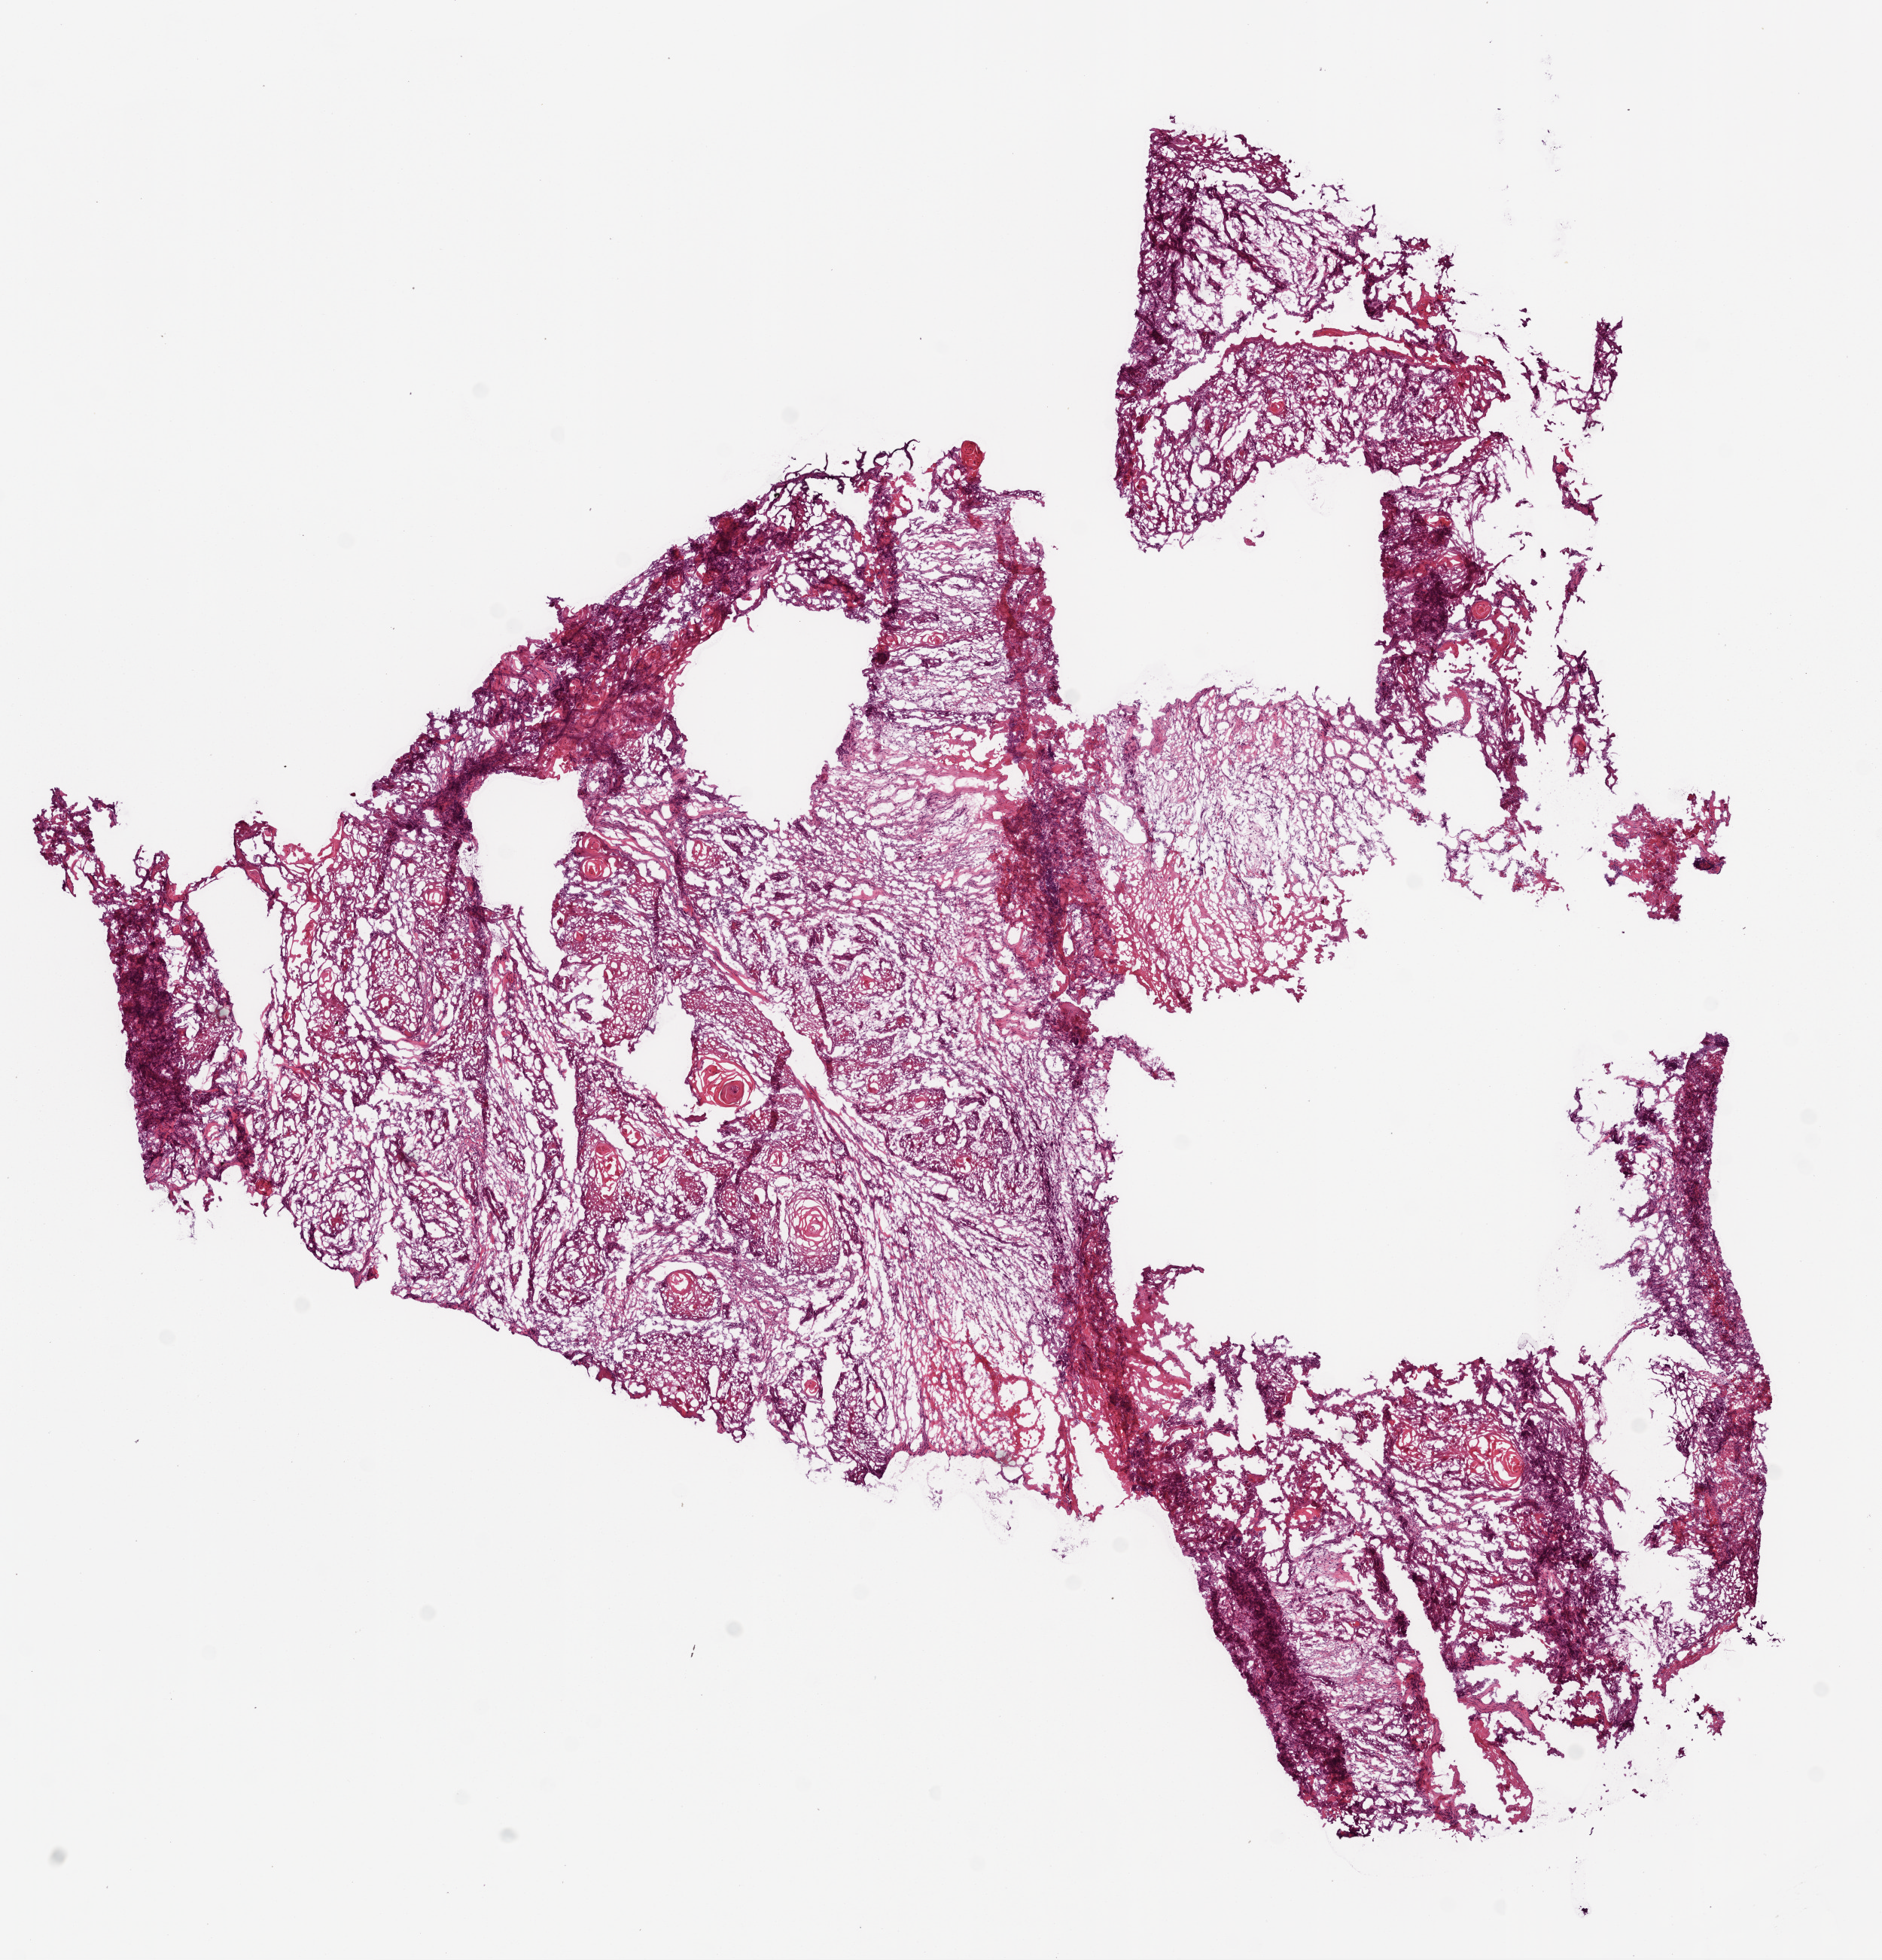
Digitized Hematoxylin and eosin (H&E) stained tissue section (whole slide) — shown as a low-resolution overview of the whole scanned area (about 10.0 x 10.4 mm), frozen section from the bottom of the tissue portion, sample: primary tumour, head and neck. Male patient; age at initial diagnosis 51 years. Histologic grade: G2 (moderately differentiated). Pathologist review of this section (percent, as recorded): tumour cells 75%, tumour nuclei 80%, normal cells 0%, stromal cells 25%, necrosis 0%.
AJCC pathologic stage: IVA. Histologic diagnosis: Squamous cell carcinoma, NOS (larynx, NOS).